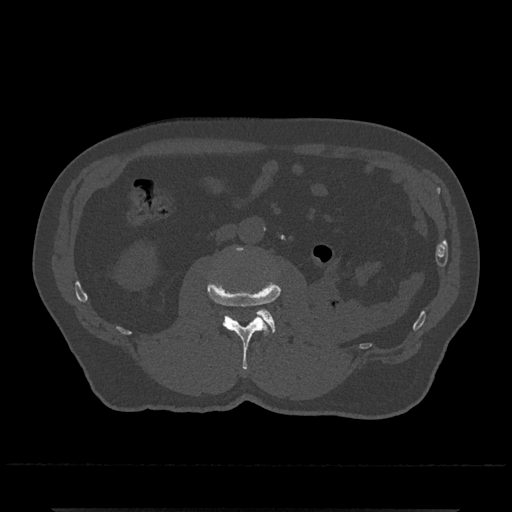
CT including the spine, one axial slice. Slice 274 of 797 in the series (ordered by position). Reconstruction kernel Br40s/3. 120 kVp. Bone window (W 1800 / L 400 HU). 0.5 mm slice thickness. 512 × 512 image matrix. Patient: male, 67 years. Case-level facts recorded for this patient, not image findings: primary cancer: prostate.
Annotated regions visible in this slice (semi-automatic segmentation, software-assisted and operator-edited):
- L2 vertebra: bounding box (x1, y1, x2, y2) in pixels: (208, 247, 280, 370)
- L3 vertebra: (257, 309, 276, 332)